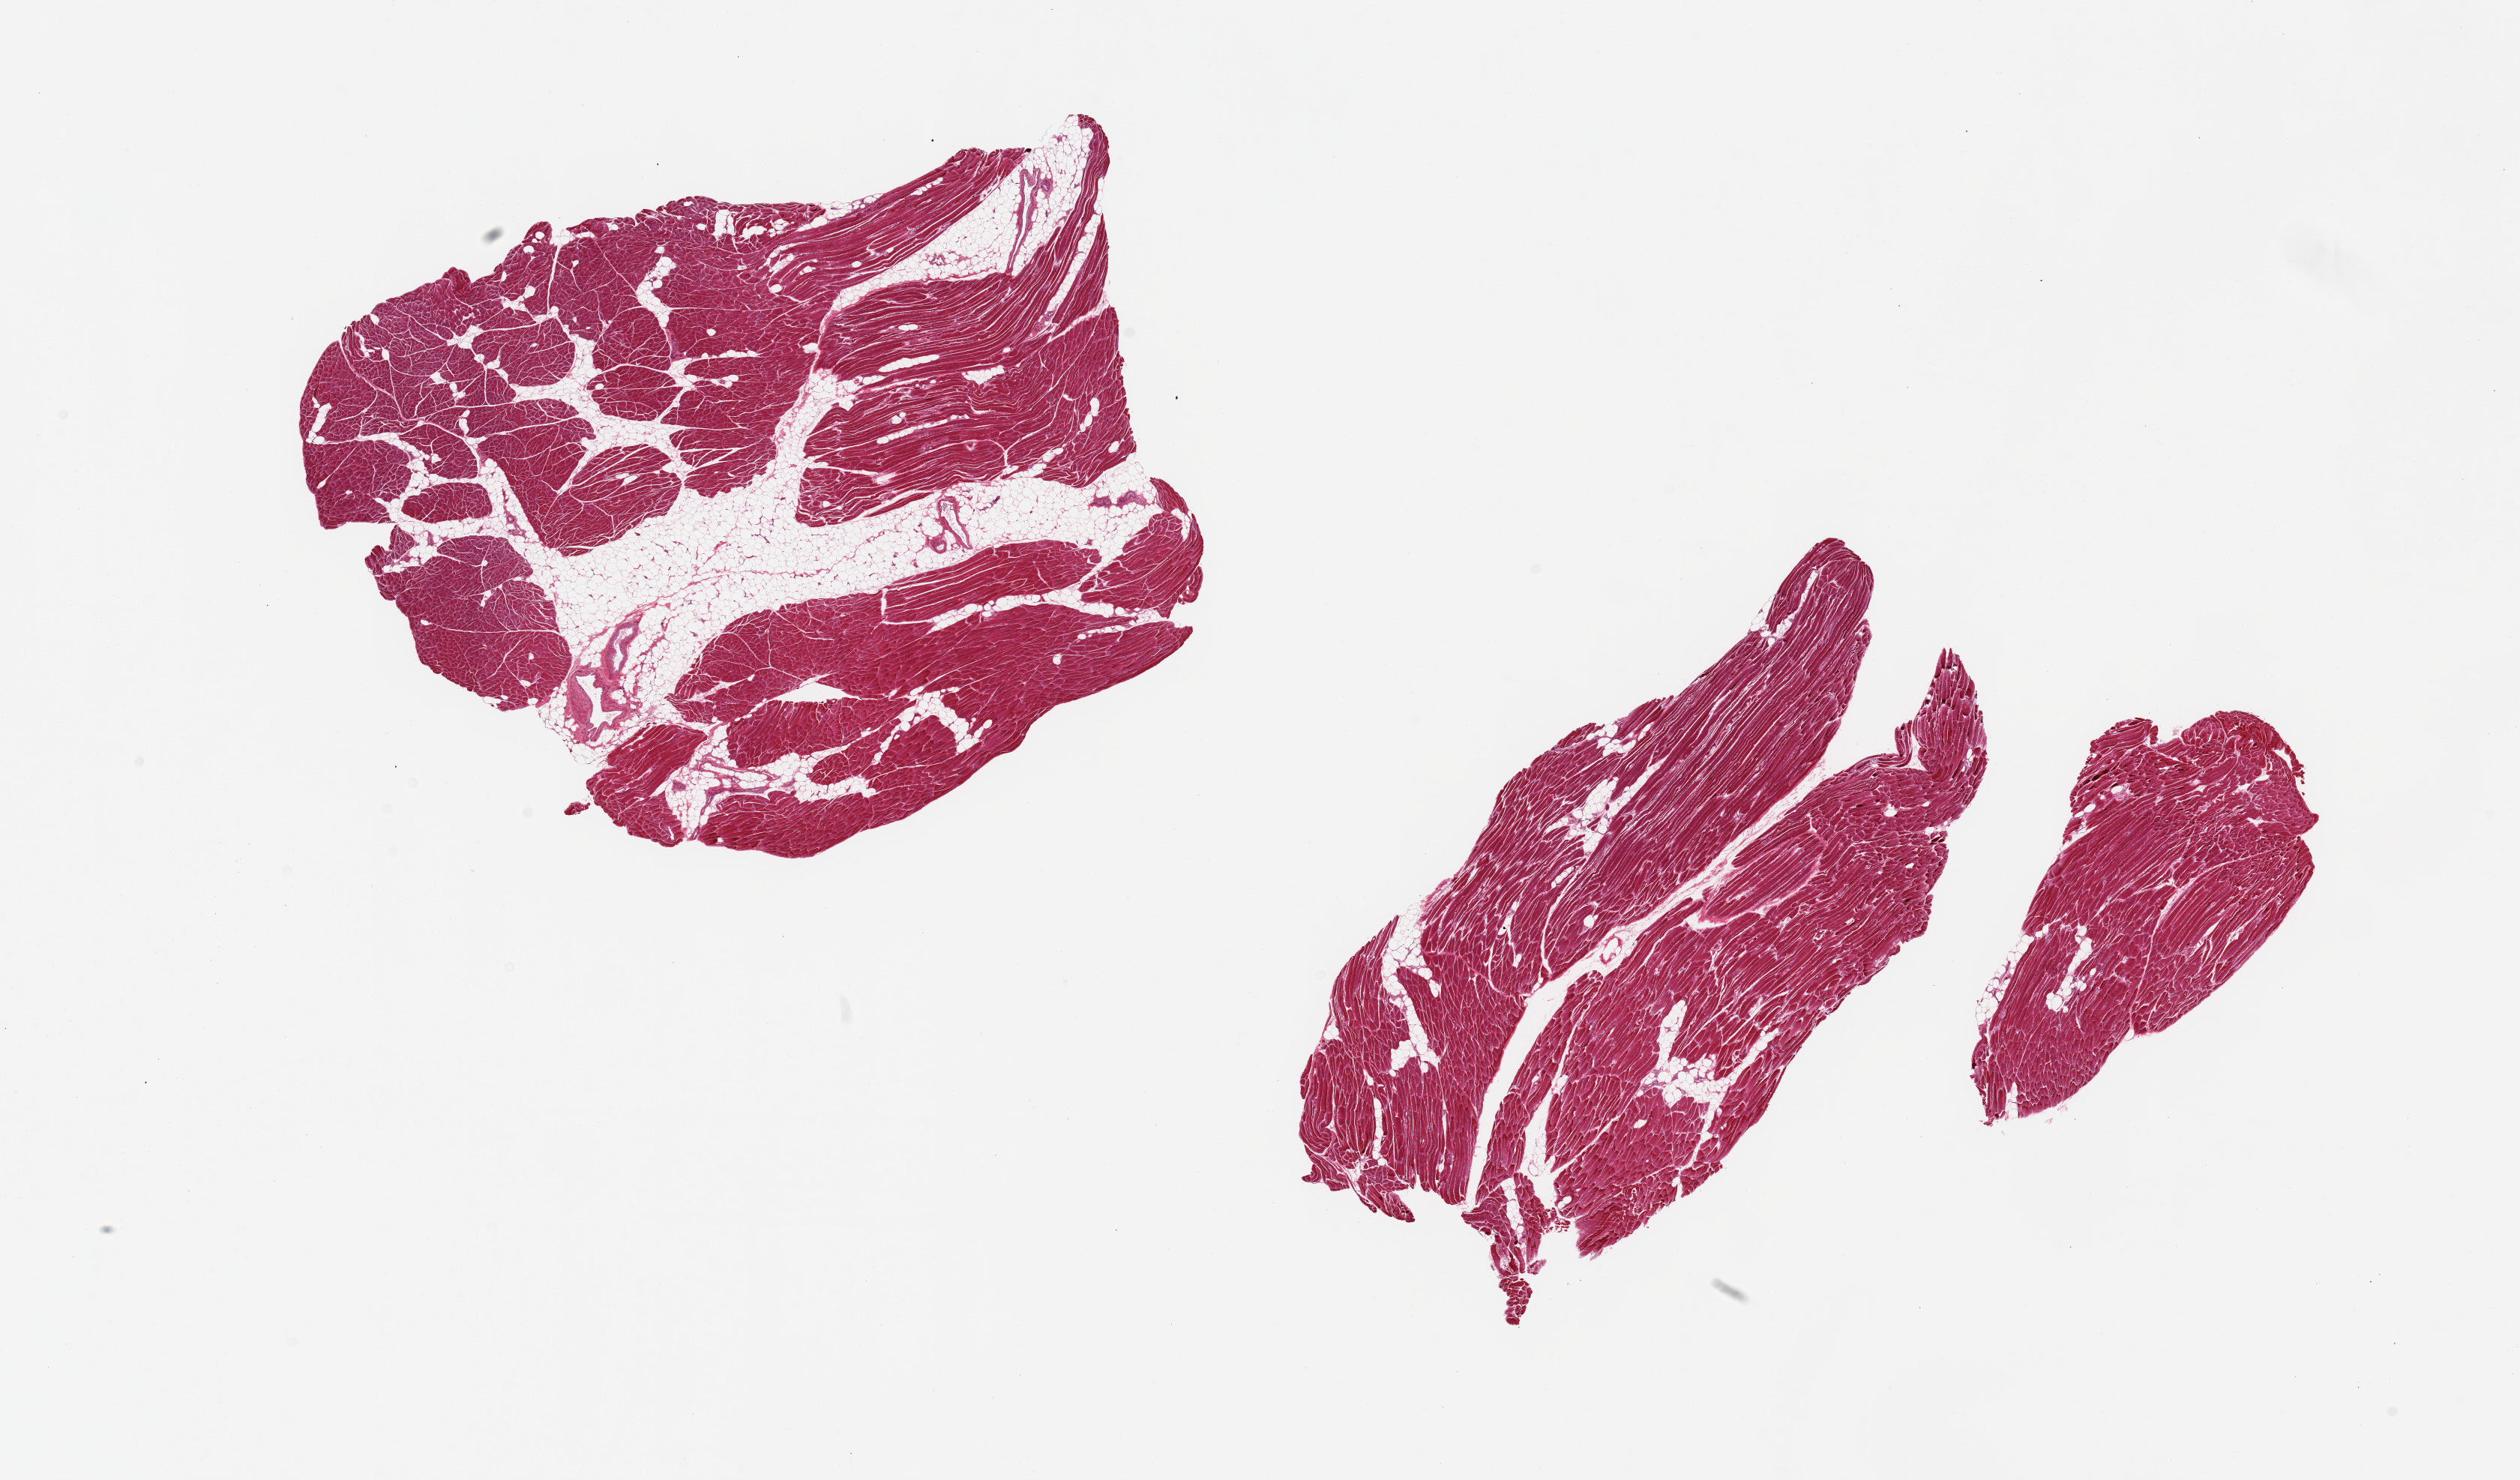
Digitized H&E-stained section, brightfield, a low-resolution overview of the entire scanned area, about 26.6 x 15.6 mm. PAXgene-fixed paraffin-embedded (PFPE) section. Section of skeletal muscle (target tissue). Tissue donor sample. Donor: male.
Review note (as recorded): 2 pieces; slight atrophy; 1 piece with 30% internal fat; other <5% fat.